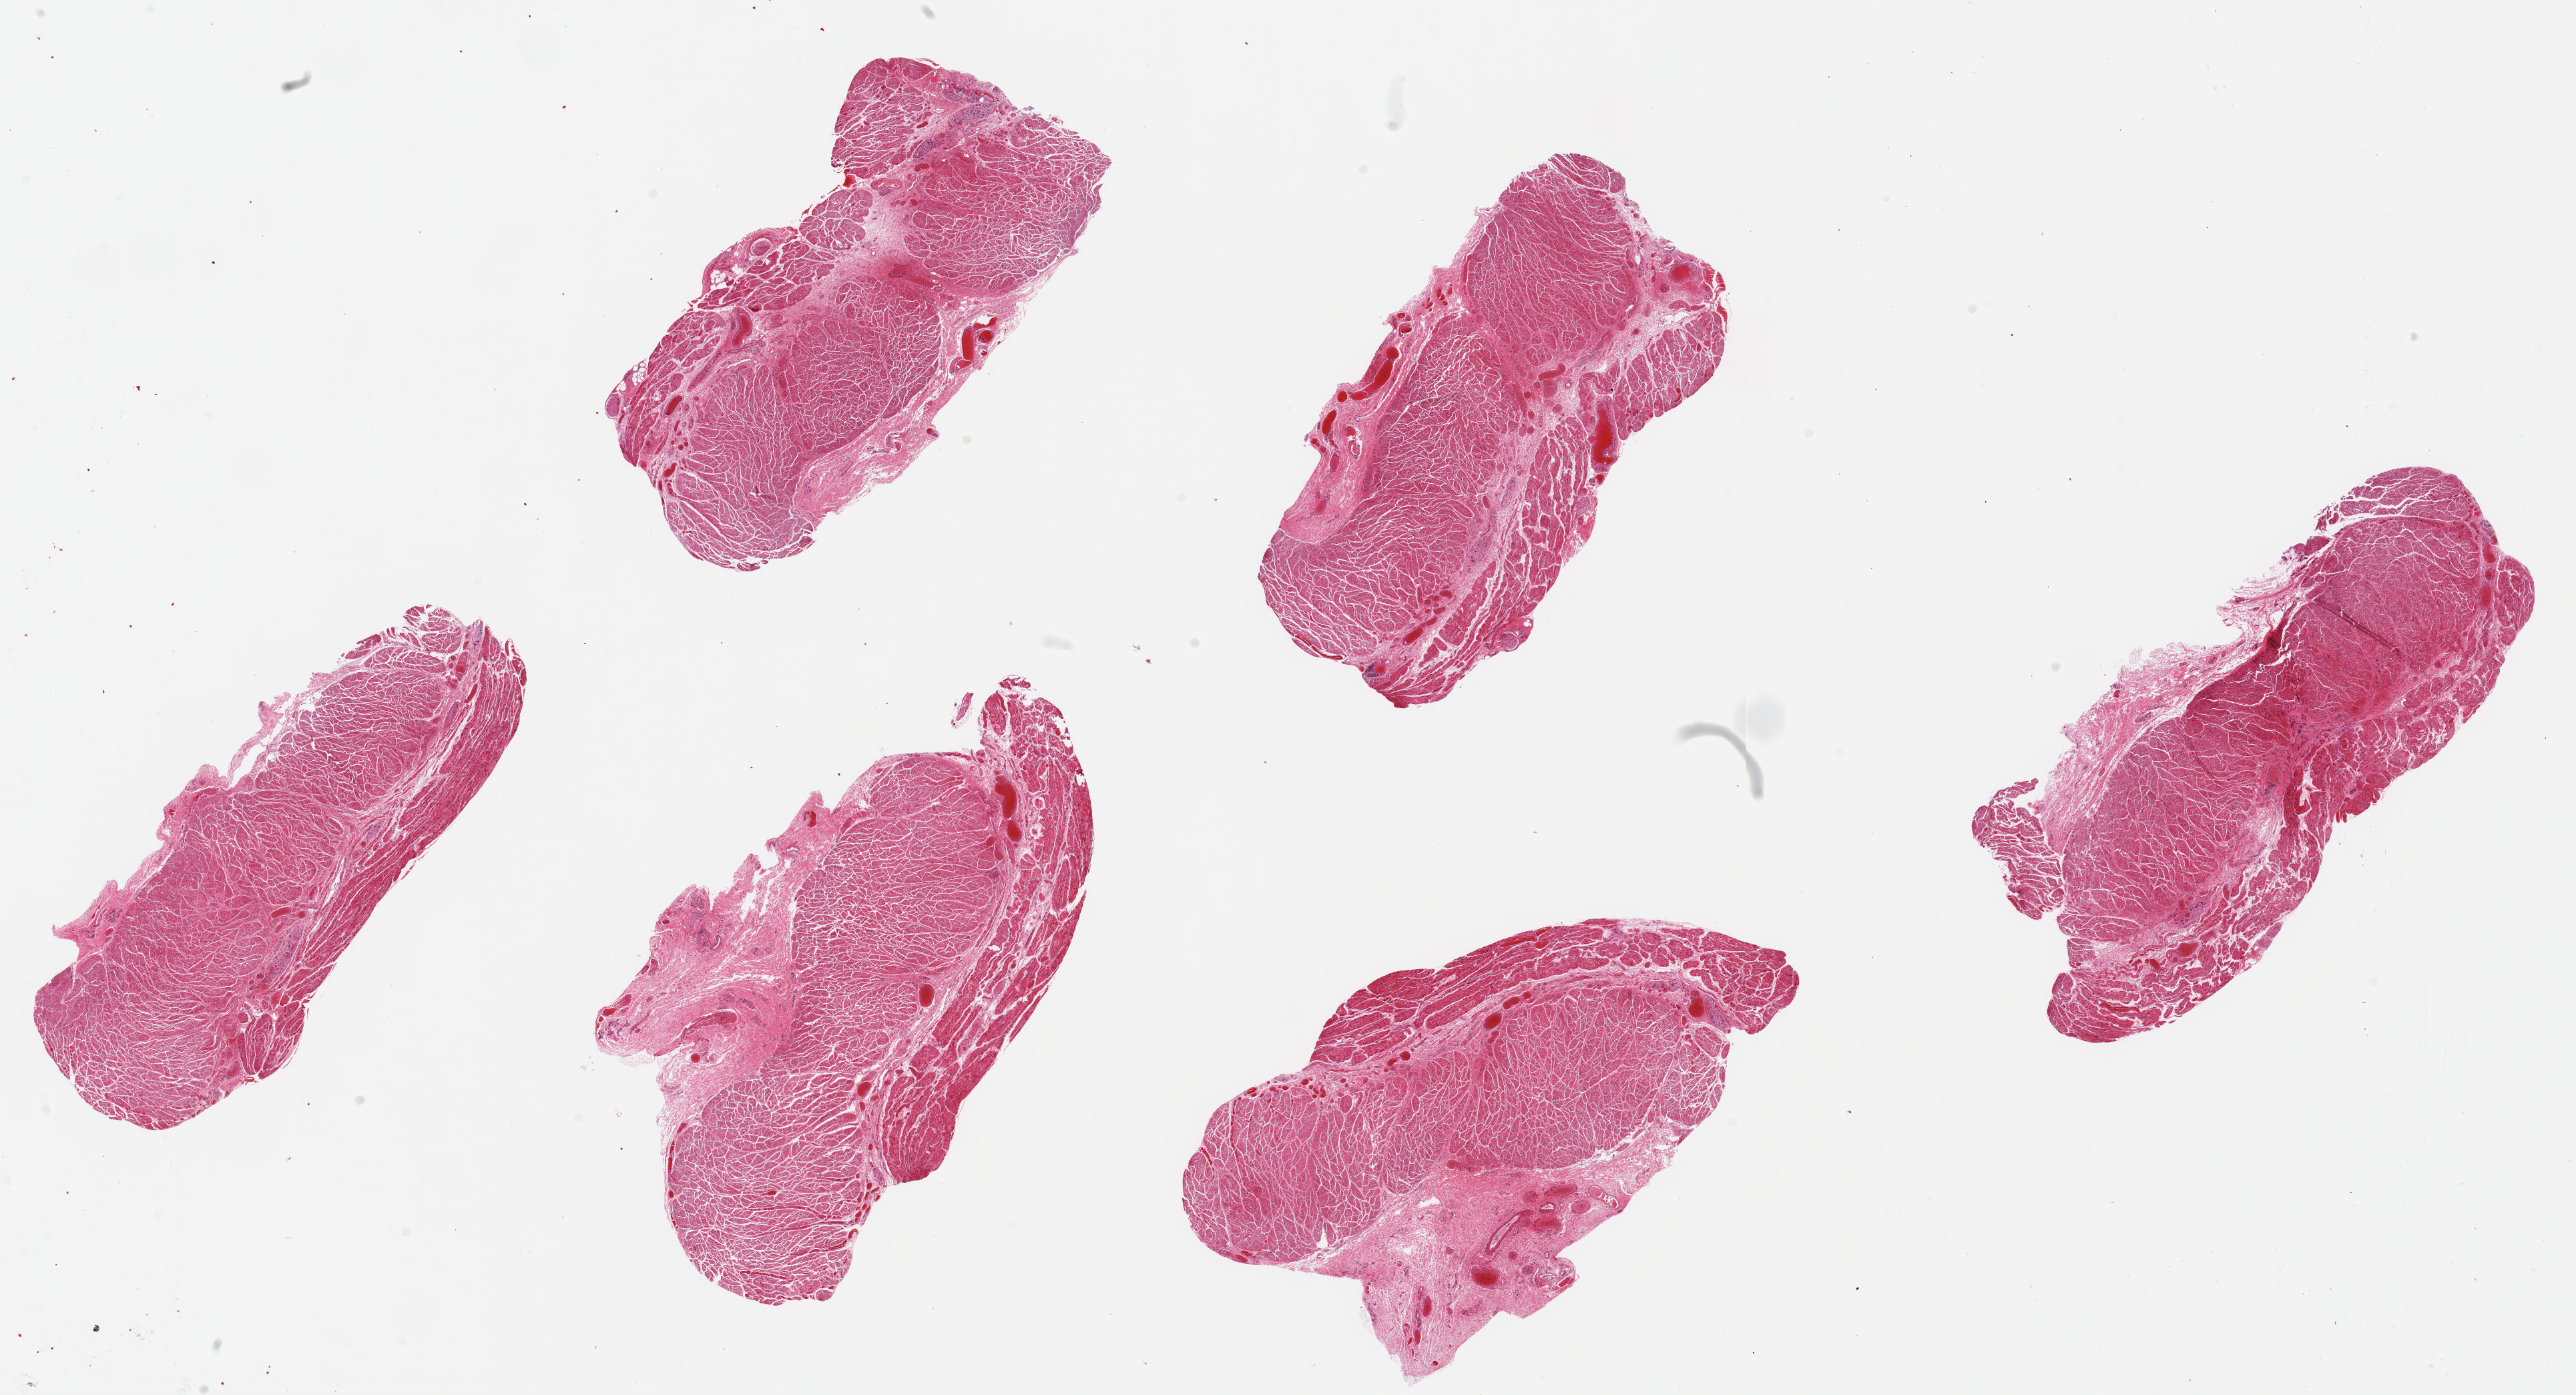
Whole-slide image, H&E stain, low-resolution overview of the scanned area, about 30.5 x 16.5 mm; PAXgene-fixed paraffin-embedded (PFPE) section; section of esophageal muscle (target tissue); donor tissue sample. Donor: male.
Review note (as recorded): 6 pieces, up to 8x5mm; all muscularis.